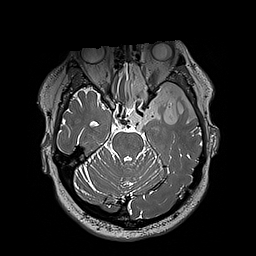
Brain MRI from a brain-tumour surgery series, one axial slice; position 137 of 192 along the scan axis; 1 mm slice thickness; 256 × 256 image matrix, field of view 250 × 250 mm. Case-level facts recorded for this patient, not image findings: histopathology: Oligodendroglioma; WHO grade: 3; IDH mutation: yes; tumour location: Left Sylvian Fissure (Temporal).
Structures marked on this image (expert manual segmentation):
- tumour: box from (x=124, y=65) to (x=197, y=125) px